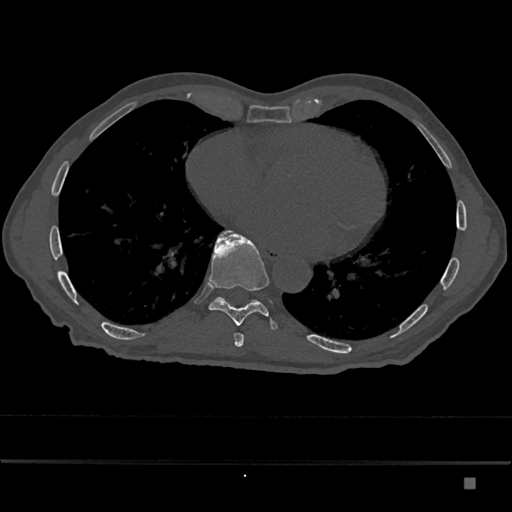
CT including the spine, one axial slice; slice 796 of 797 in the series (ordered by position); 120 kVp; bone window (W 1800 / L 400 HU); 512 × 512 image matrix, field of view 390 × 390 mm. Male patient, age 72 years. From the clinical record (not read from this slice): primary cancer: prostate.
Structures marked on this image (semi-automatic segmentation, software-assisted and operator-edited):
- T10 vertebra: bounding box [x1, y1, x2, y2] px = [216, 297, 259, 303]
- T9 vertebra: [209, 231, 277, 329]